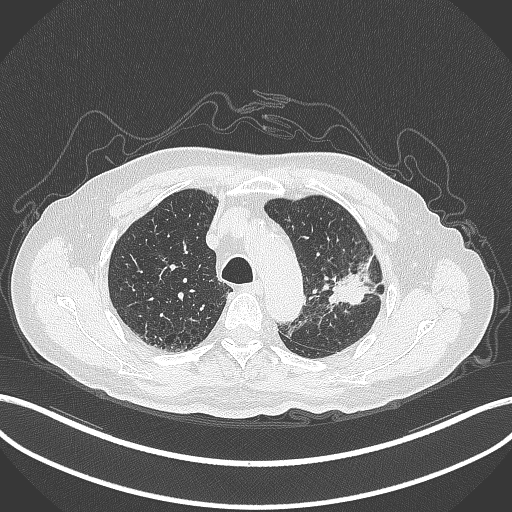
Chest CT, one axial slice; position 226 of 331 along the scan axis; 120 kVp; lung window (W 1500 / L -600 HU); 1 mm slice thickness; 512 × 512 image matrix, field of view 400 × 400 mm. Male patient, age 79 years. From the clinical record (not read from this slice): clinical TNM (as recorded): T2a N1 M1.
Outlined on this slice (rectangle marked by the reading radiologist):
- lung tumour (recorded histology: adenocarcinoma): bounding box (x1, y1, x2, y2) in pixels: (331, 253, 384, 311)